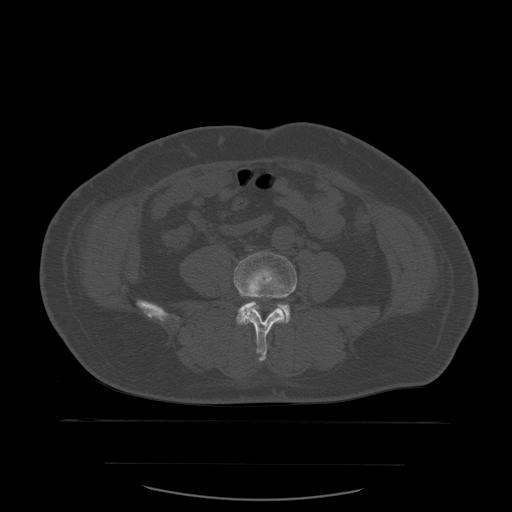
CT including the spine, one axial slice; slice 157 of 590 in the series (ordered by position); bone window (W 1800 / L 400 HU); 512 × 512 image matrix, field of view 479 × 479 mm. Patient age 71 years. From the clinical record (not read from this slice): primary cancer: lung; vertebrae with lytic lesions (as recorded): T1, T2, L5, S1.
Outlined on this slice (semi-automatic segmentation, software-assisted and operator-edited):
- L4 vertebra: bounding box [x1, y1, x2, y2] px = [234, 252, 297, 362]
- L5 vertebra: [236, 297, 290, 325]